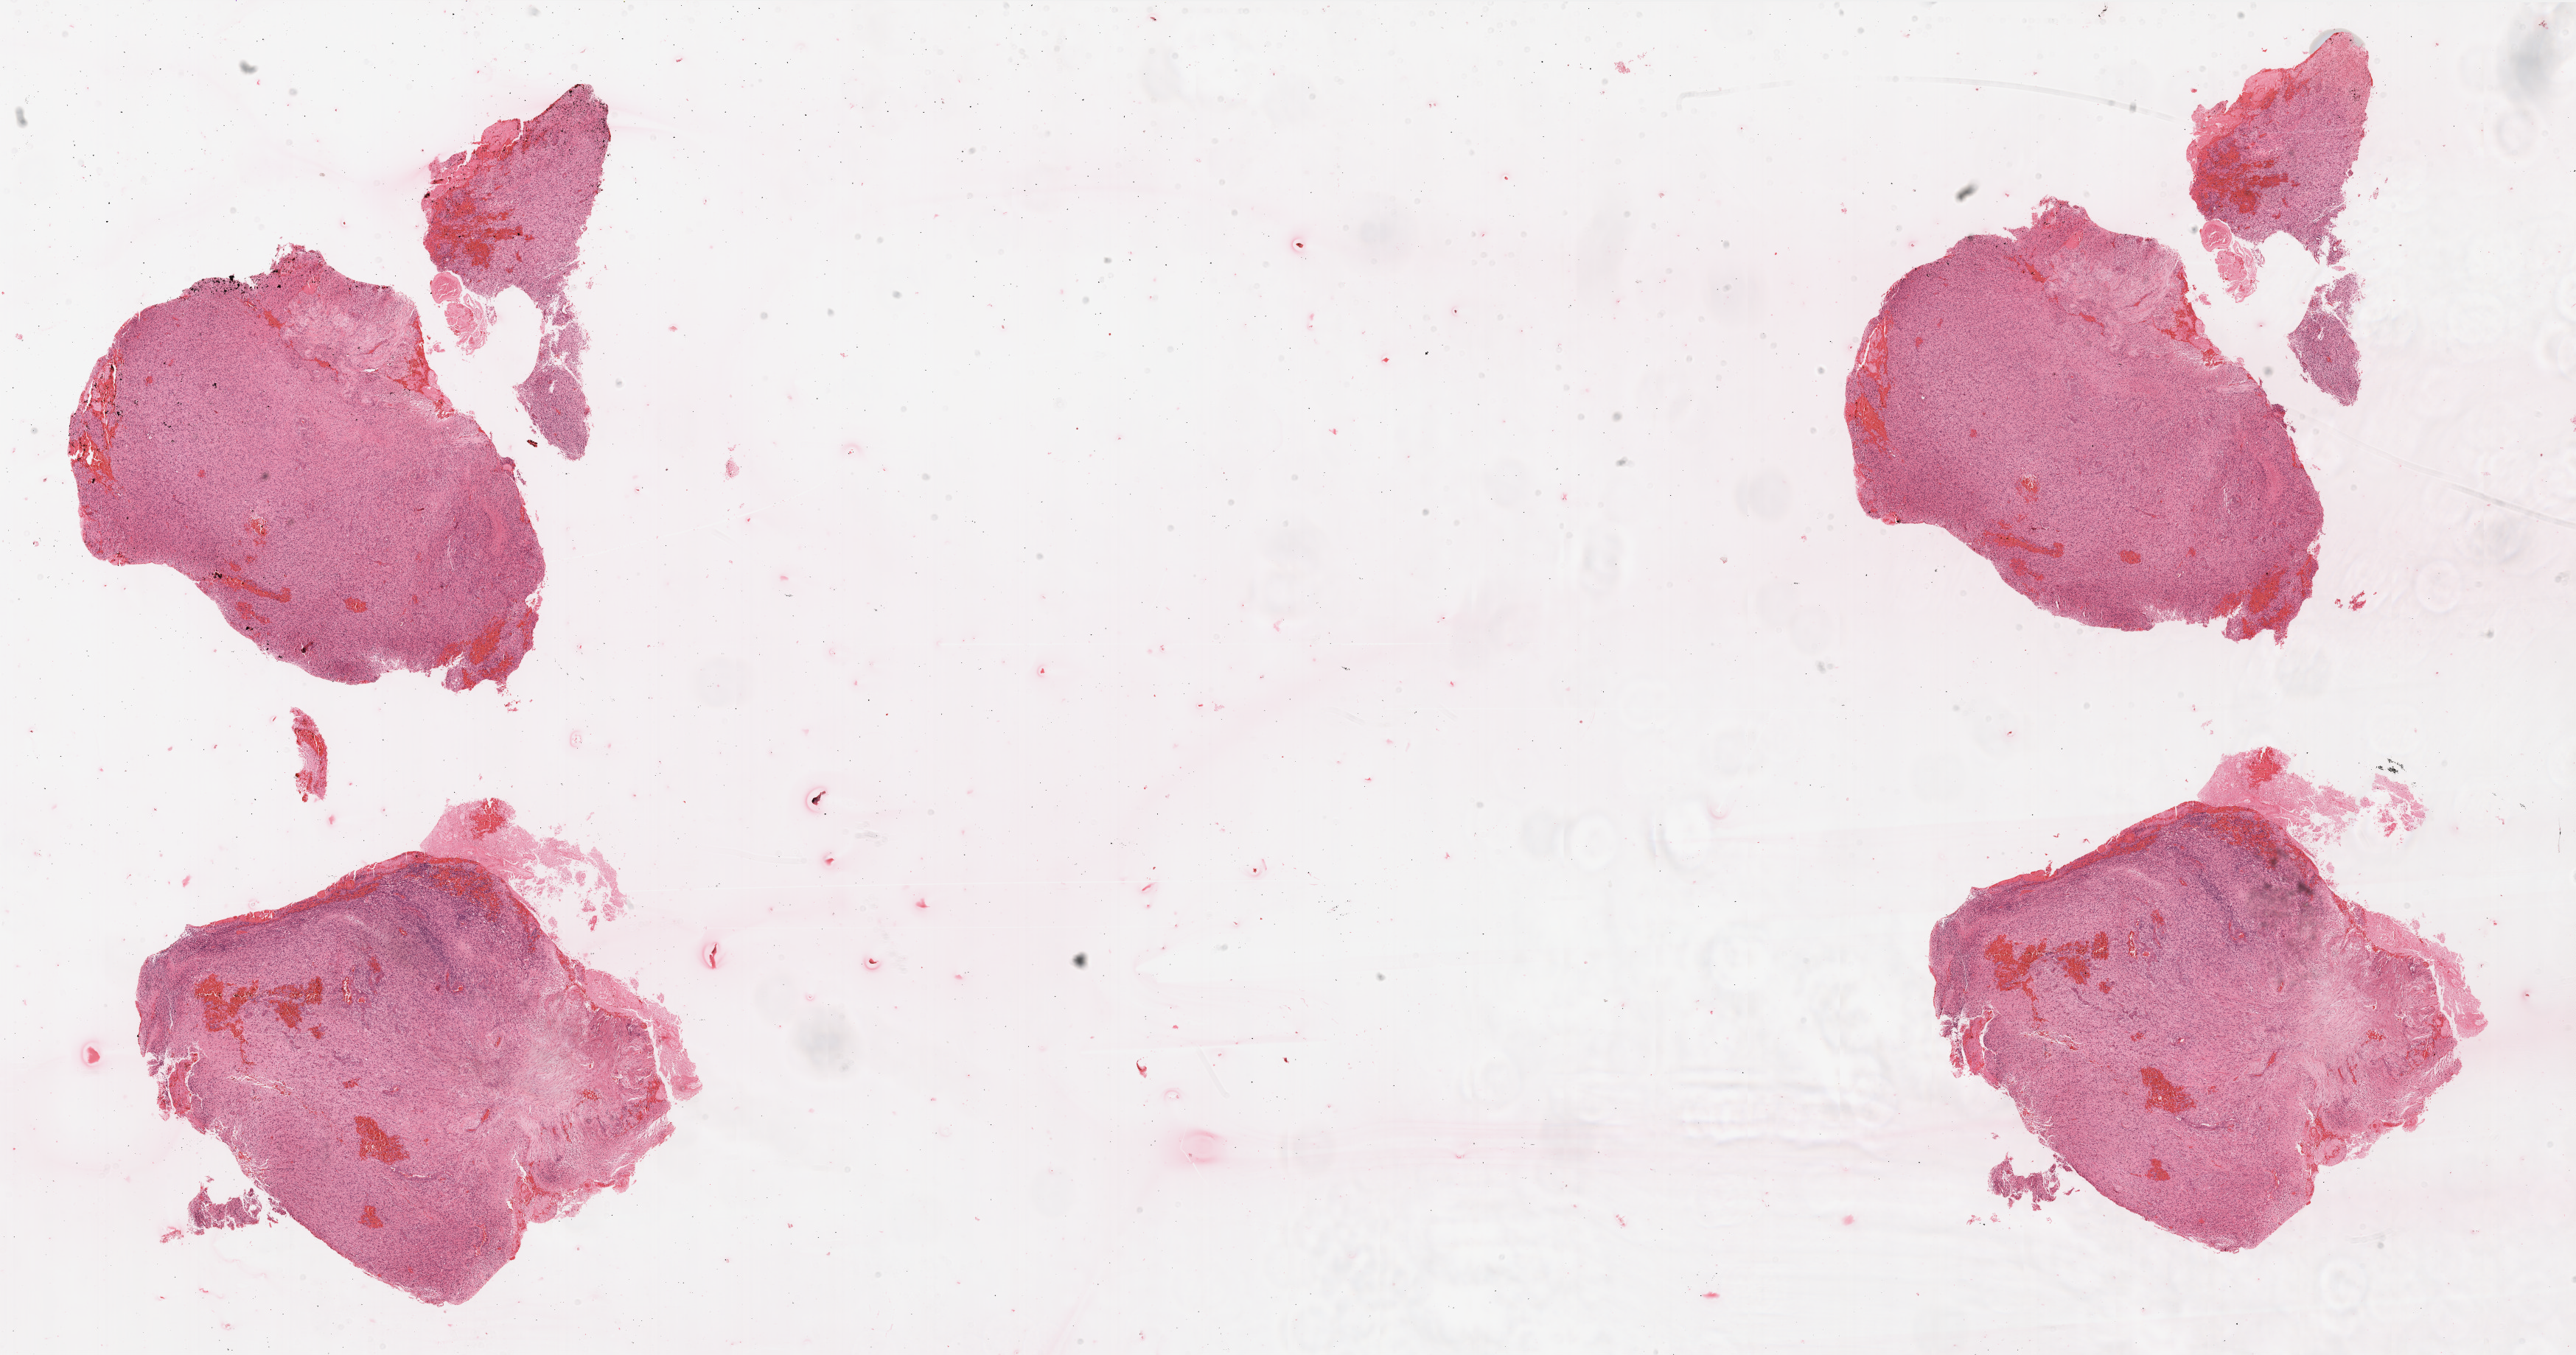
H&E-stained whole-slide image, low-resolution overview of the scanned area, about 28.0 x 14.7 mm; FFPE section; brain, primary tumour sample. Patient: male, age at initial diagnosis 67 years.
• histologic diagnosis: Glioblastoma